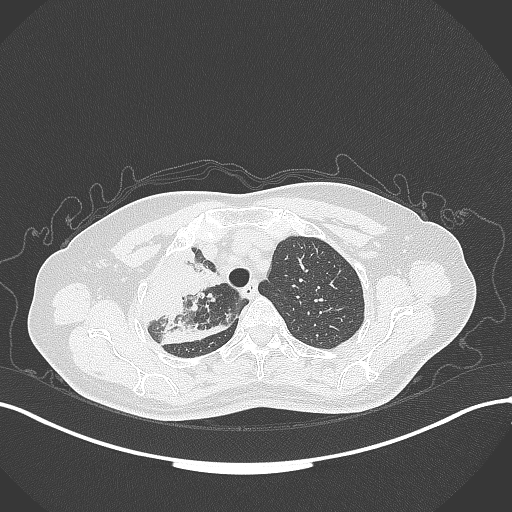
Chest CT, one axial slice; slice 256 of 309 in the series (ordered by position); reconstruction kernel B70f; 120 kVp; lung window (W 1500 / L -600 HU); 1 mm slice thickness; 512 × 512 image matrix, field of view 400 × 400 mm. Patient: female, 60 years. Case-level facts recorded for this patient, not image findings: clinical TNM (as recorded): T3 N1 M1.
Annotated regions visible in this slice (bounding box drawn by a radiologist):
- lung tumour (recorded histology: adenocarcinoma): bounding box [x1, y1, x2, y2] px = [130, 241, 223, 322]